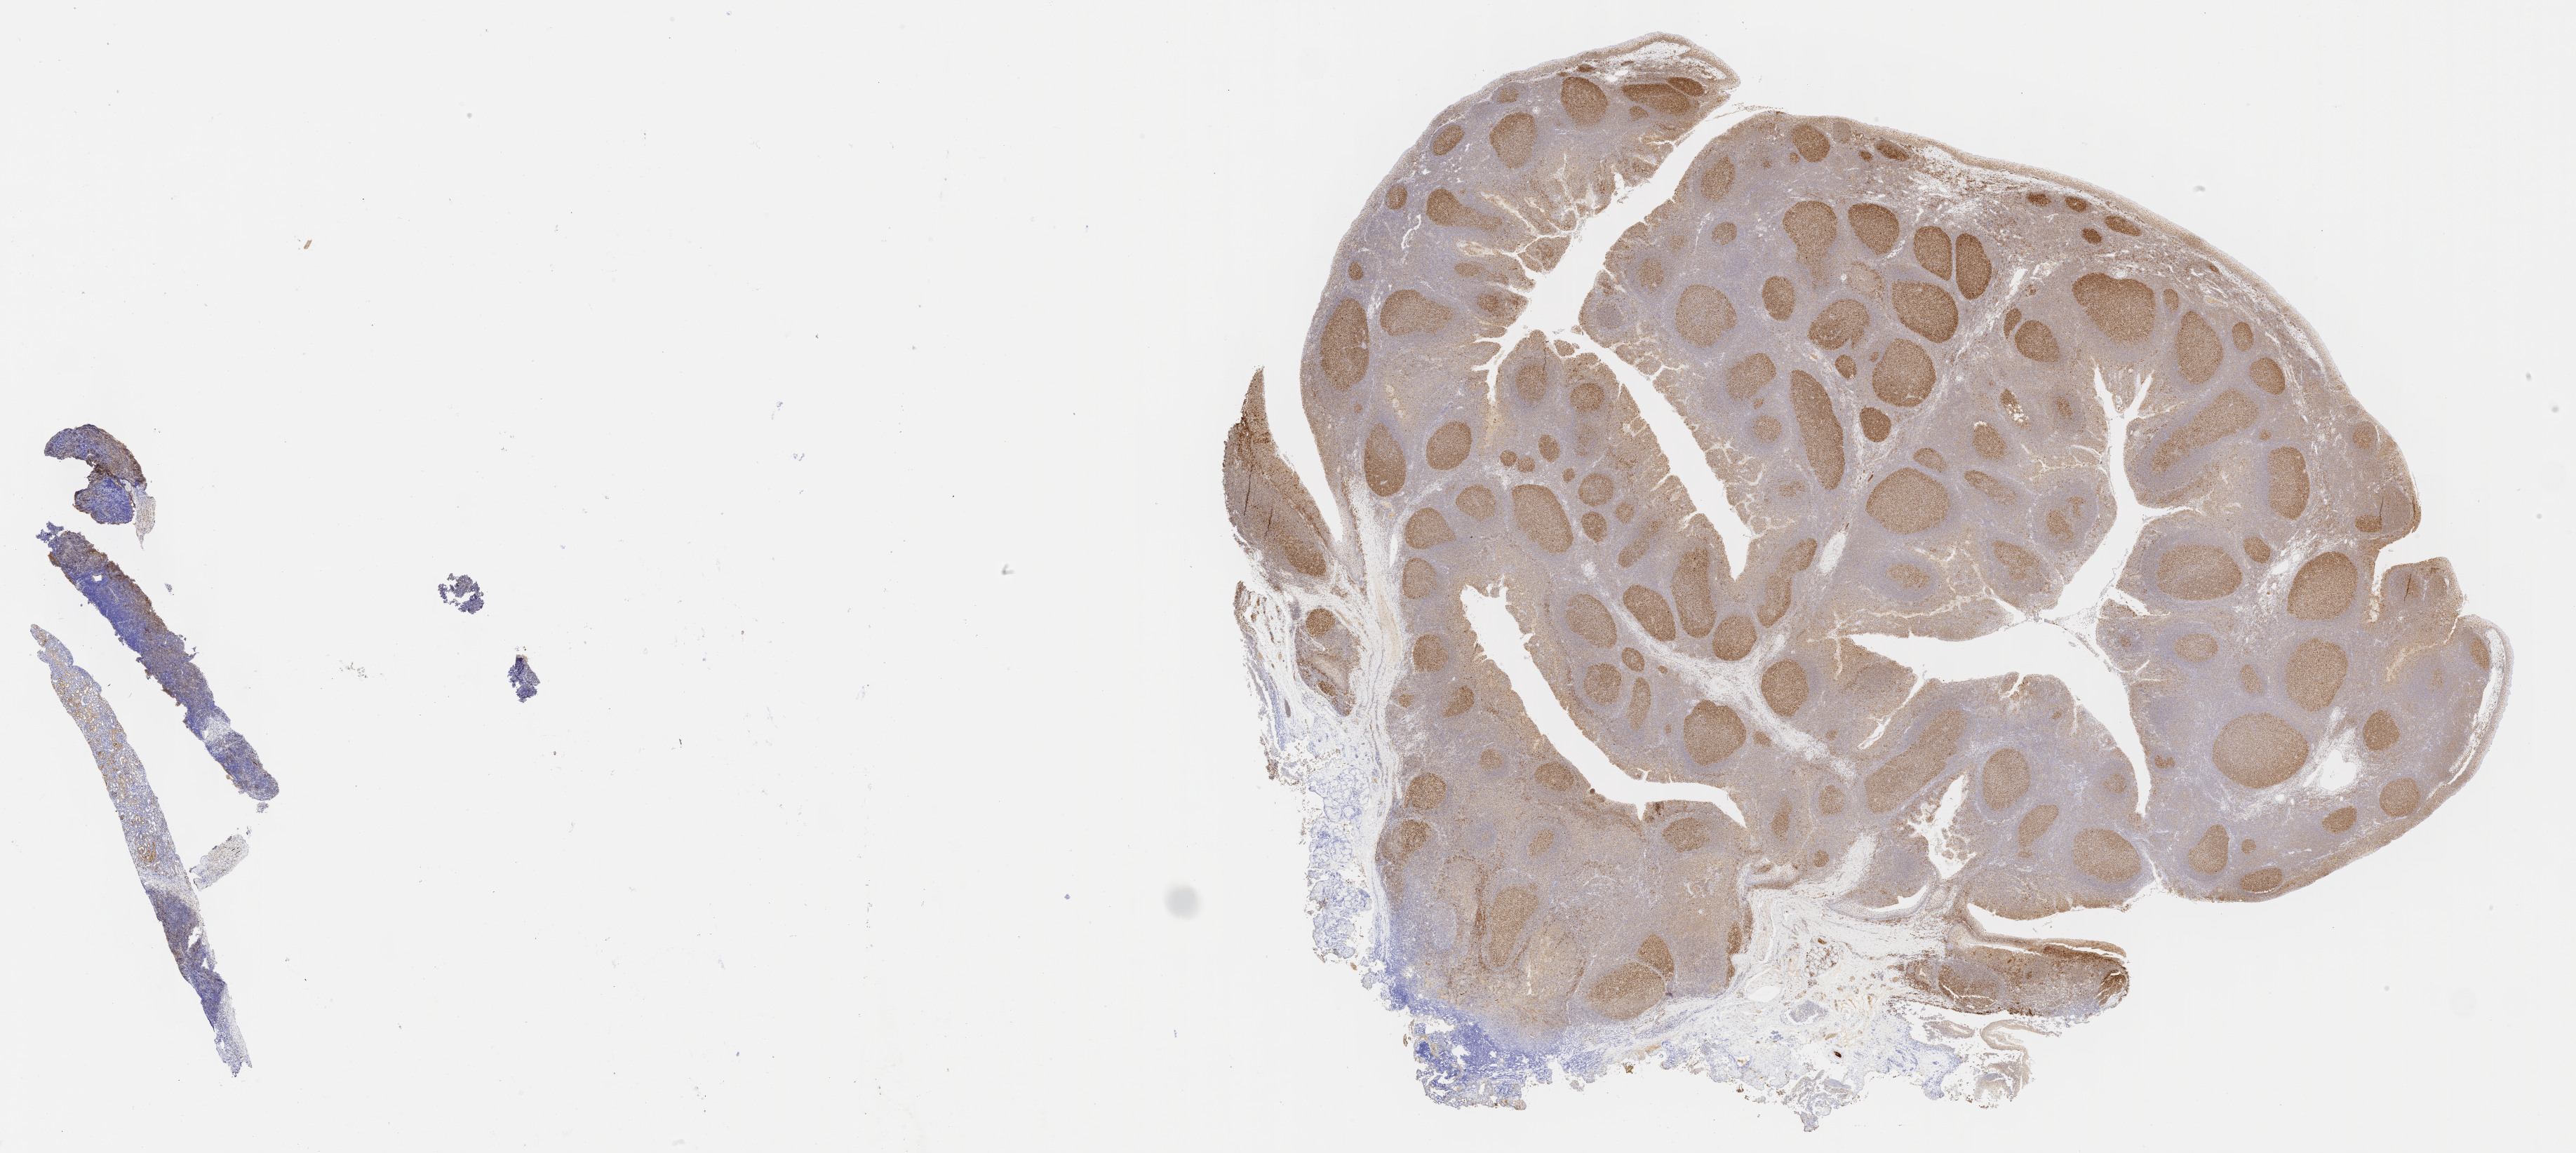
Whole-slide image, immunohistochemical stain for BCL6 — whole scanned area (about 29.7 x 13.3 mm) shown as a low-resolution overview; tumor tissue; site: liver. Male patient; age at initial diagnosis 8 years.
- diagnosis: Burkitt lymphoma, NOS